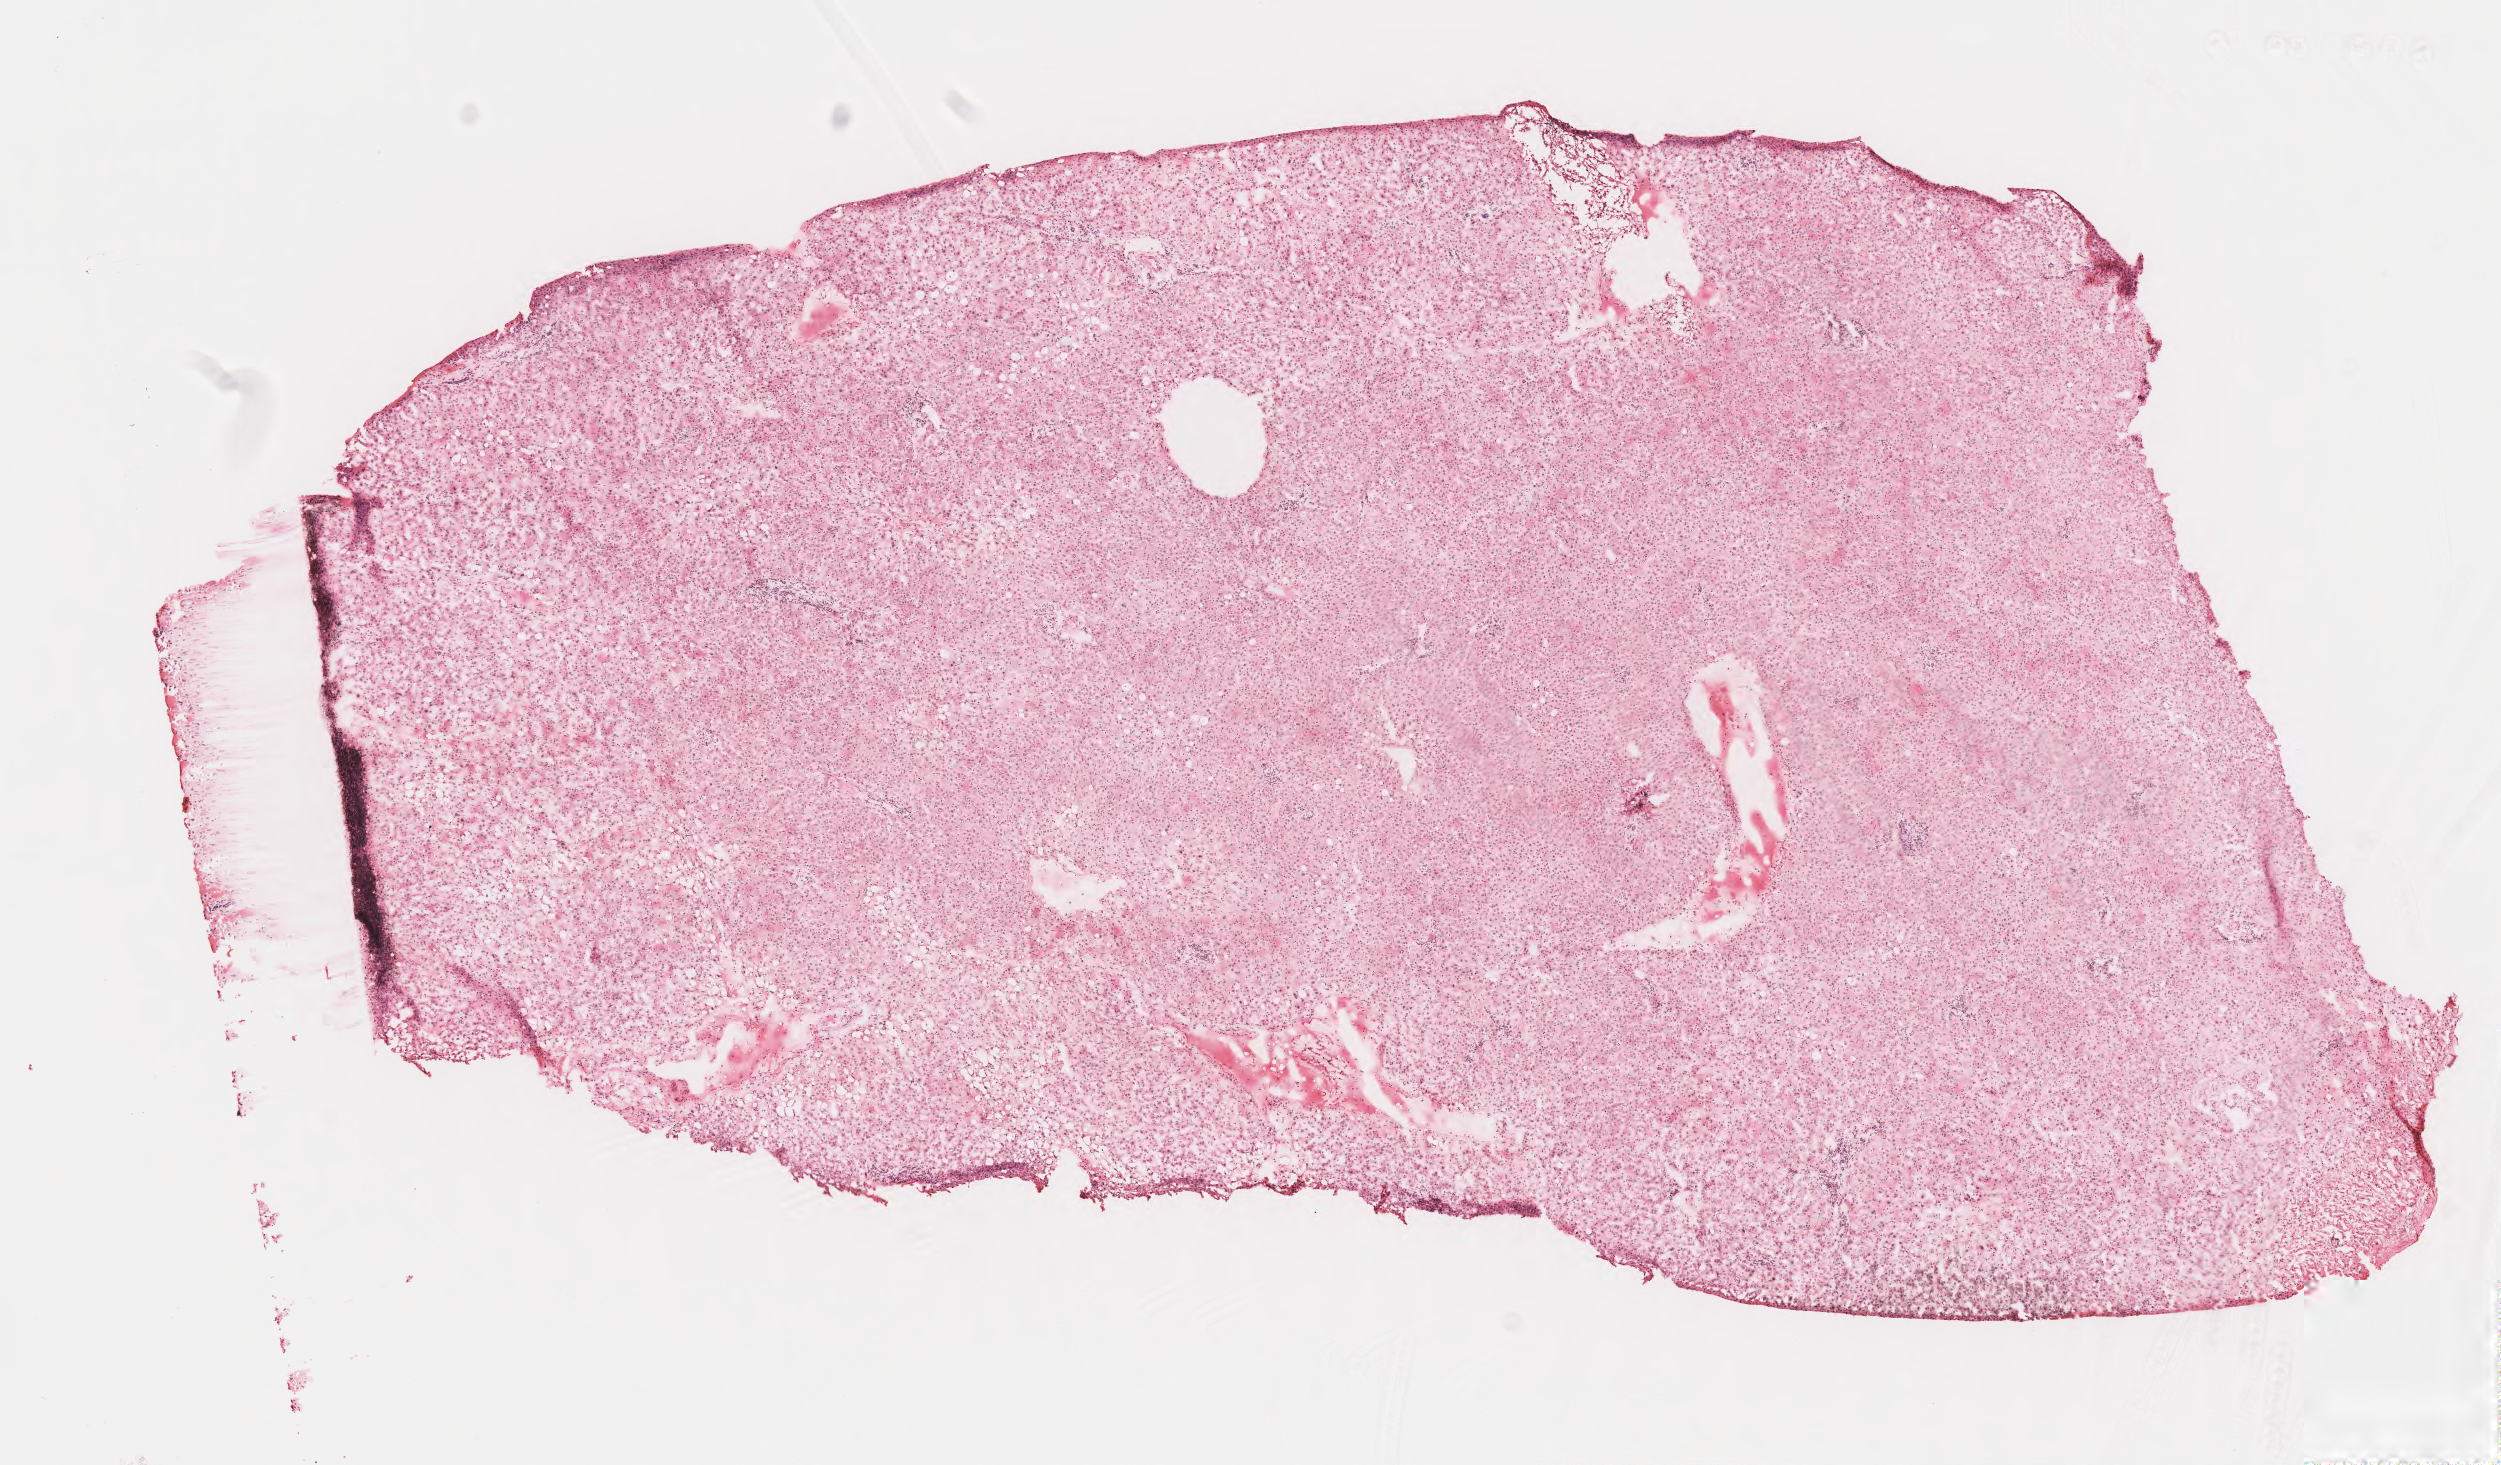
Digitized haematoxylin and eosin-stained section — a low-resolution overview of the entire scanned area, about 9.9 x 5.8 mm. Frozen section (tissue freezing medium). Normal-tissue sample (non-tumor) from a patient with adenocarcinoma, metastatic, NOS. Male, age 47 years at initial diagnosis. Slide review estimates, as recorded: tumor cells 0%, tumor nuclei 0%, stromal cells 10%, necrosis 0%, normal cells 90%. Inflammatory infiltration, as recorded: lymphocyte infiltration 4%, monocyte infiltration 1%, neutrophil infiltration 2%.
This section: non-tumor tissue sample; the patient's diagnosis is given above.